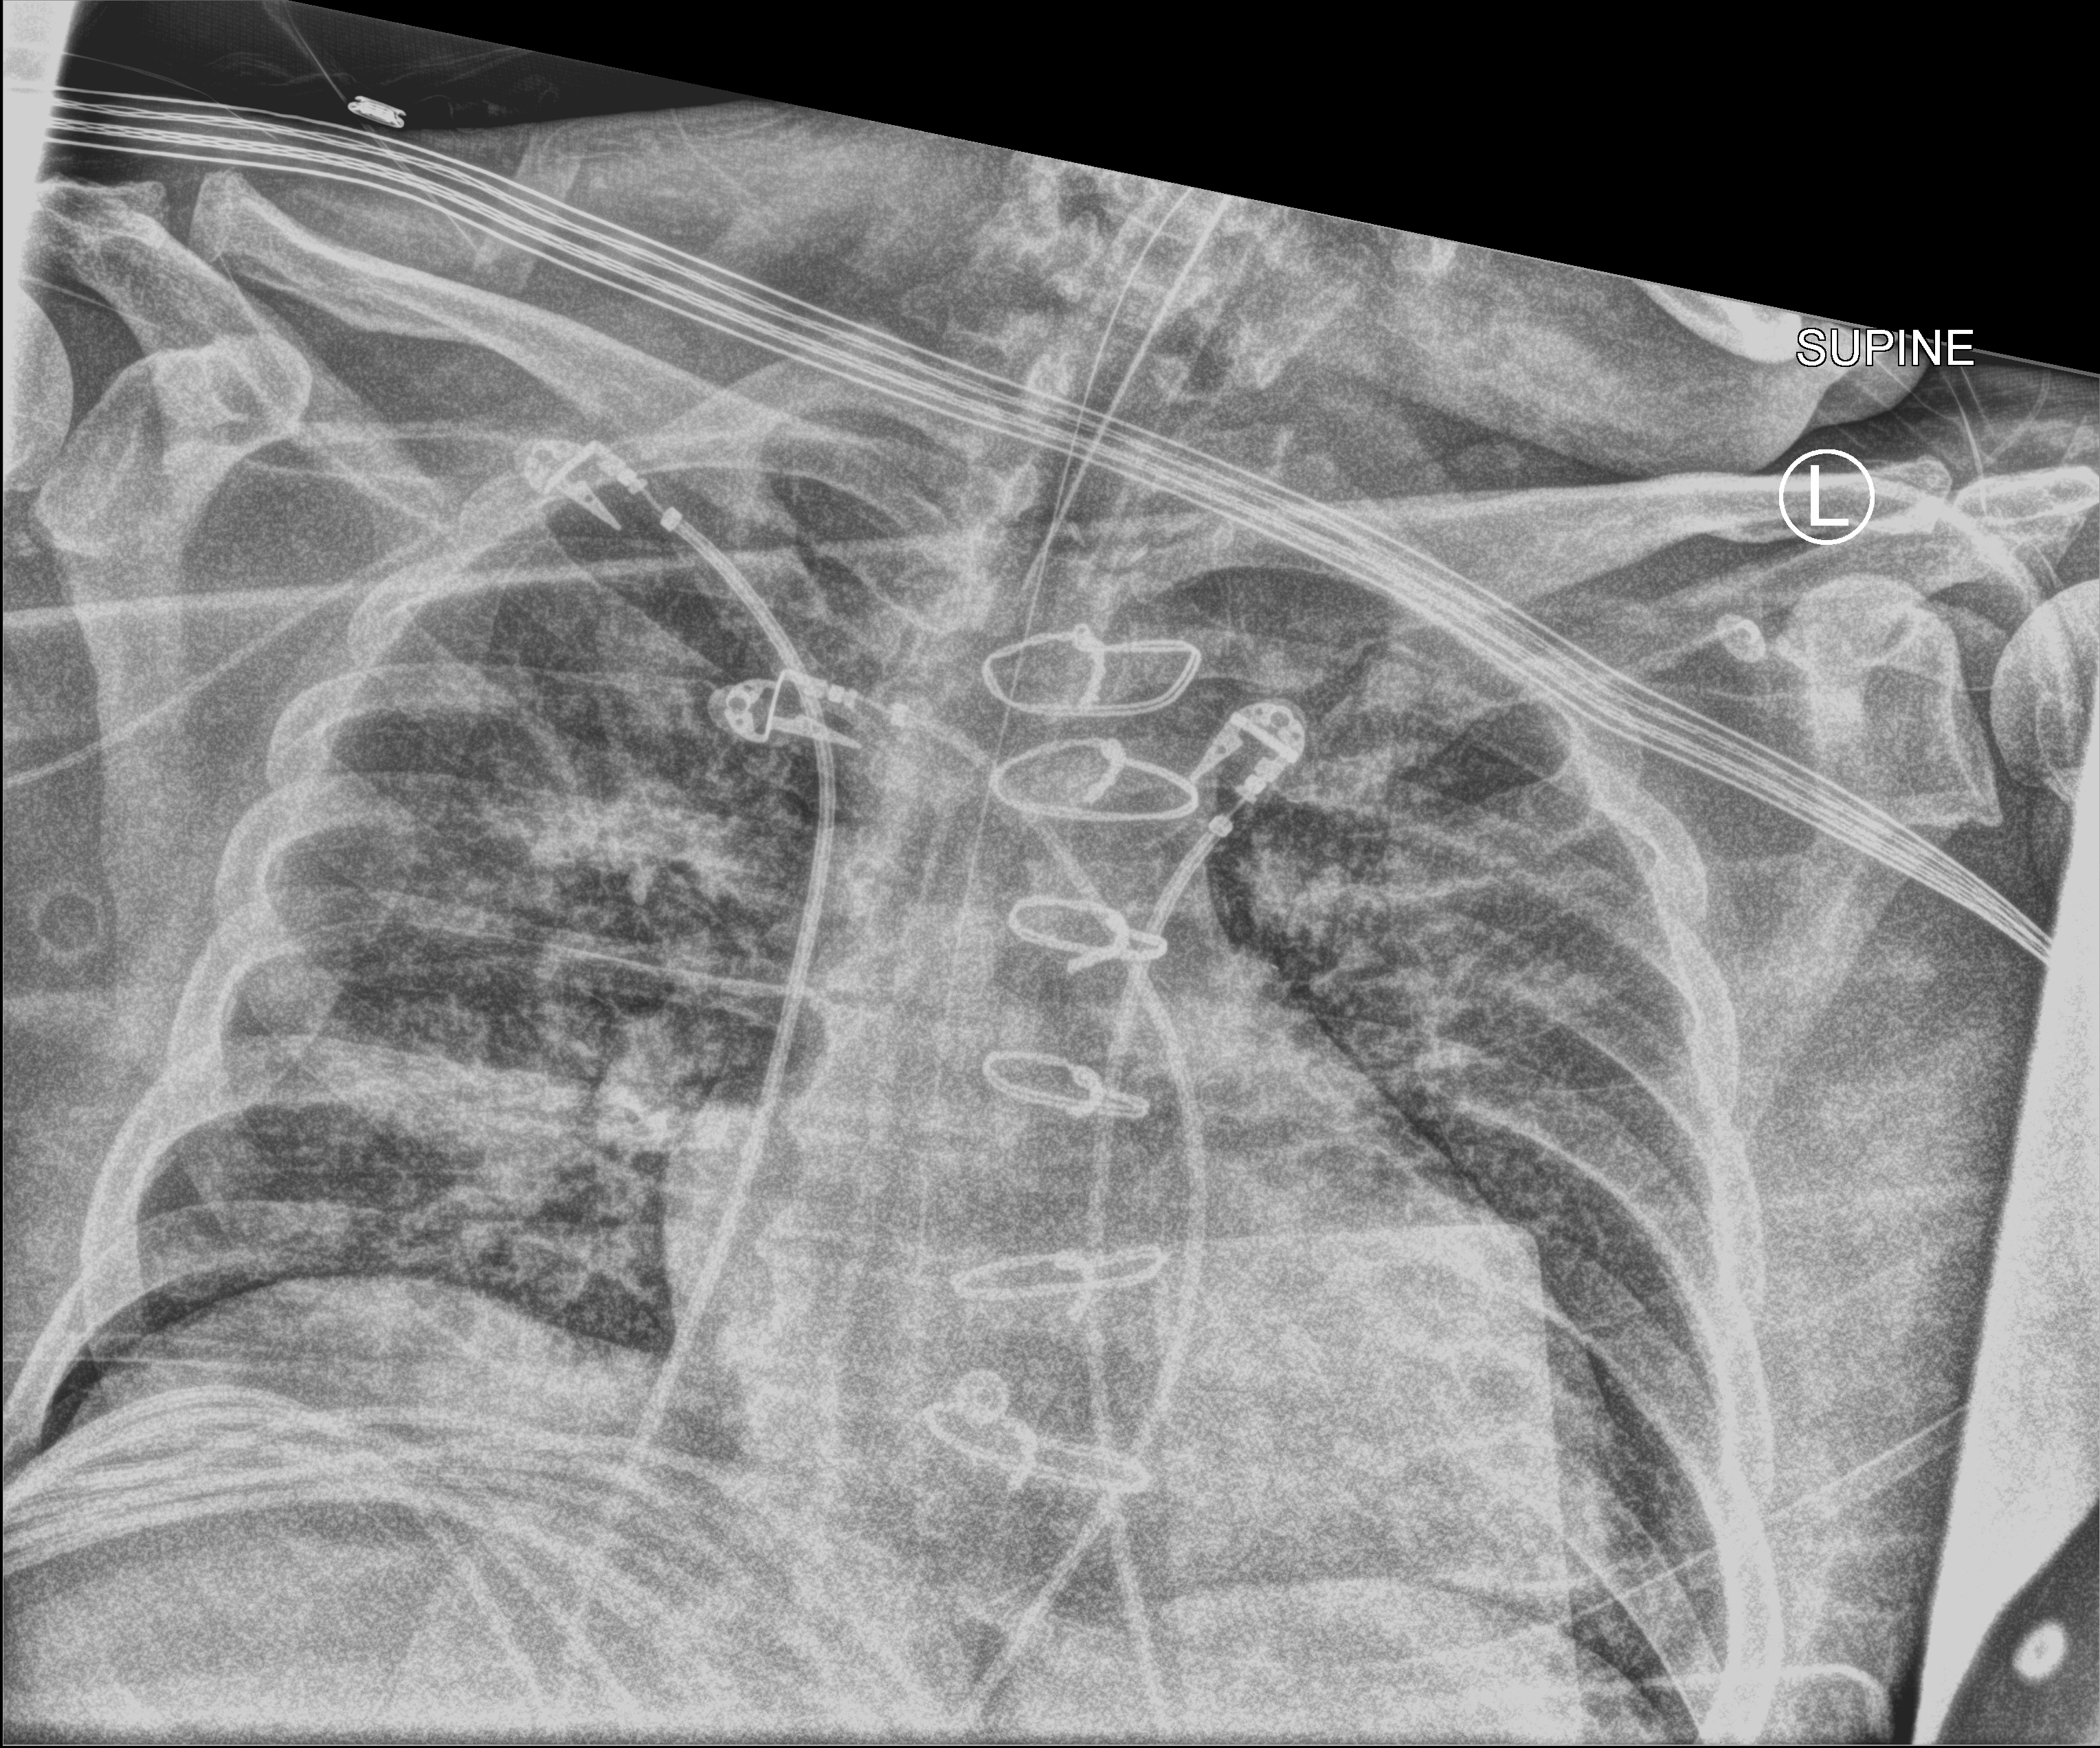
Chest X-ray (portable); anteroposterior (AP) projection. Patient hospitalised with COVID-19, aged 18–59 years.
Hospital-stay facts (about this admission, not read from this image; timing relative to this image not recorded):
- mechanically ventilated during this hospital stay: yes